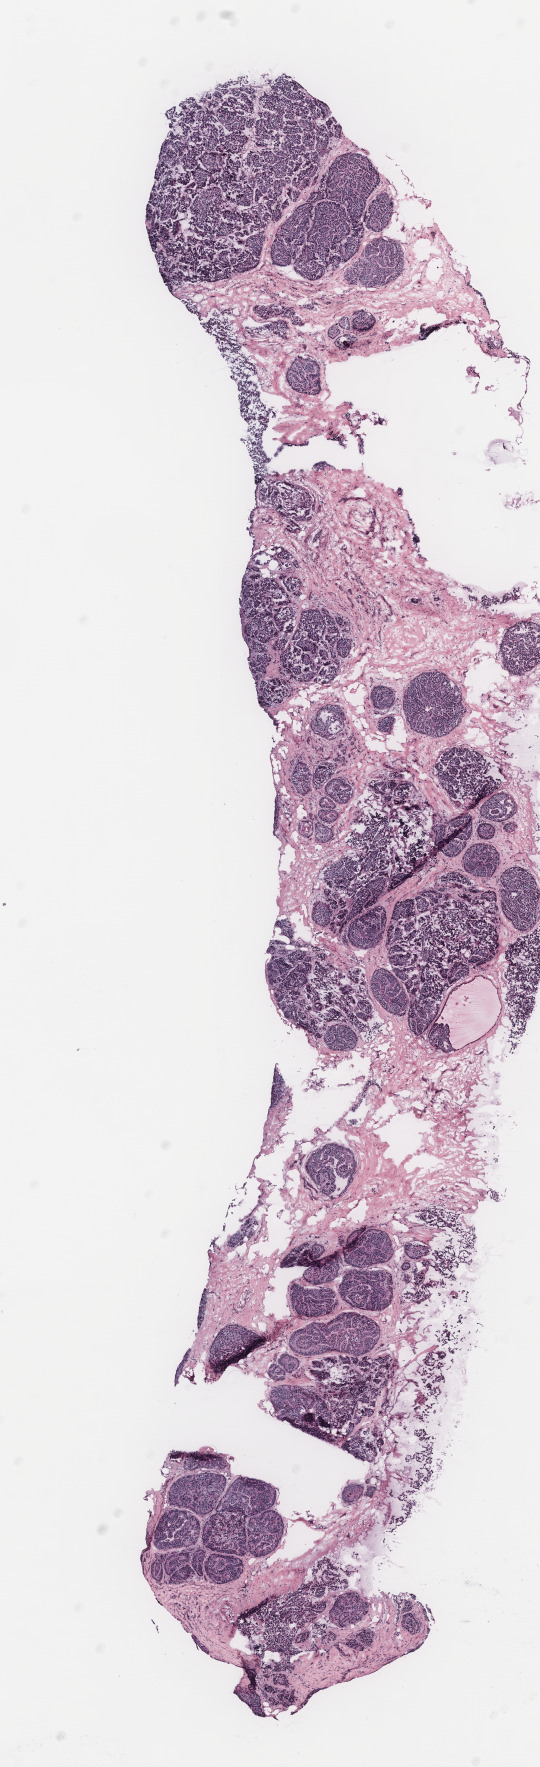
Digitized H&E tissue section (whole slide) — a low-resolution overview of the entire scanned area, about 4.3 x 14.1 mm. 52-year-old female patient.
- specimen: tumour tissue sample, breast